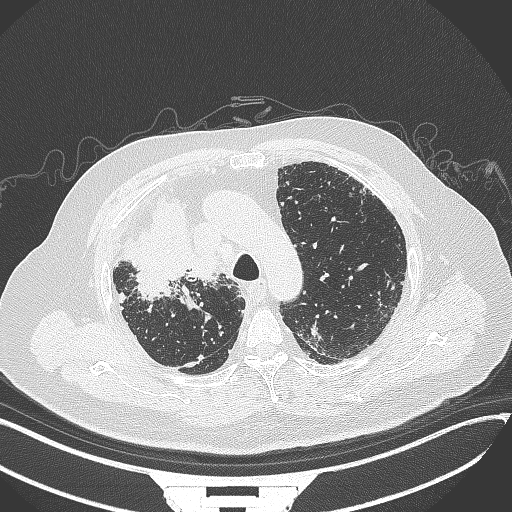
Chest CT, one axial slice; slice 266 of 384 in the series (ordered by position); reconstruction kernel B70f; lung window (W 1500 / L -600 HU); 1 mm slice thickness; 512 × 512 image matrix, field of view 400 × 400 mm. Patient: male, 69 years. From the clinical record (not read from this slice): clinical TNM (as recorded): T4 N3 M1.
Outlined on this slice (bounding box drawn by a radiologist):
- lung tumour (recorded histology: adenocarcinoma): bounding box [x1, y1, x2, y2] px = [119, 197, 219, 301]